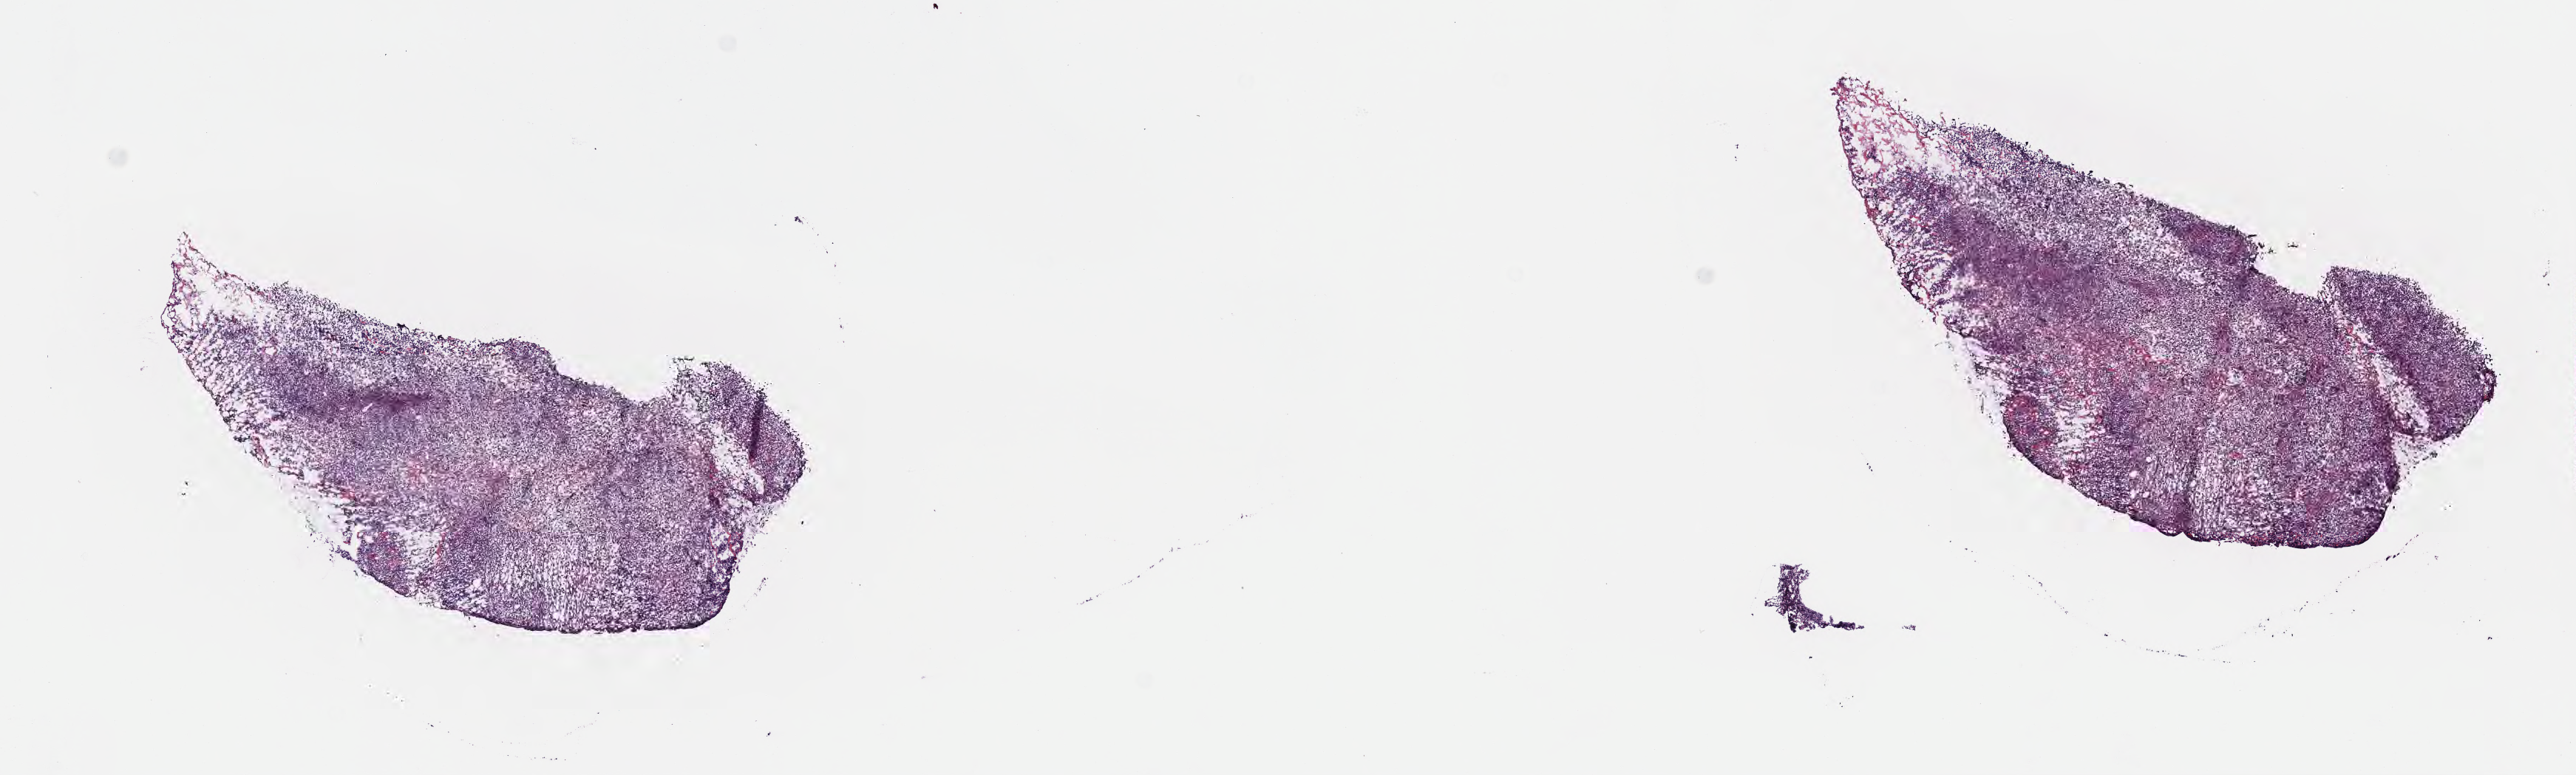
Digitized haematoxylin and eosin-stained section — whole scanned area (about 14.1 x 4.2 mm) shown as a low-resolution overview; frozen section; primary tumor; anatomic site: cranium. Male patient; age at initial diagnosis 5 years. Pathologist review of this section (percent, as recorded): tumor cells 85%, tumor nuclei 90%, stromal cells 5%, necrosis 10%, normal cells 0%. Infiltration values recorded for this section: lymphocyte infiltration 50%, monocyte infiltration 15%, neutrophil infiltration 15%.
Diagnosis: Burkitt lymphoma, NOS. Section: top of the tissue portion. Ann Arbor stage (patient): Stage IV.